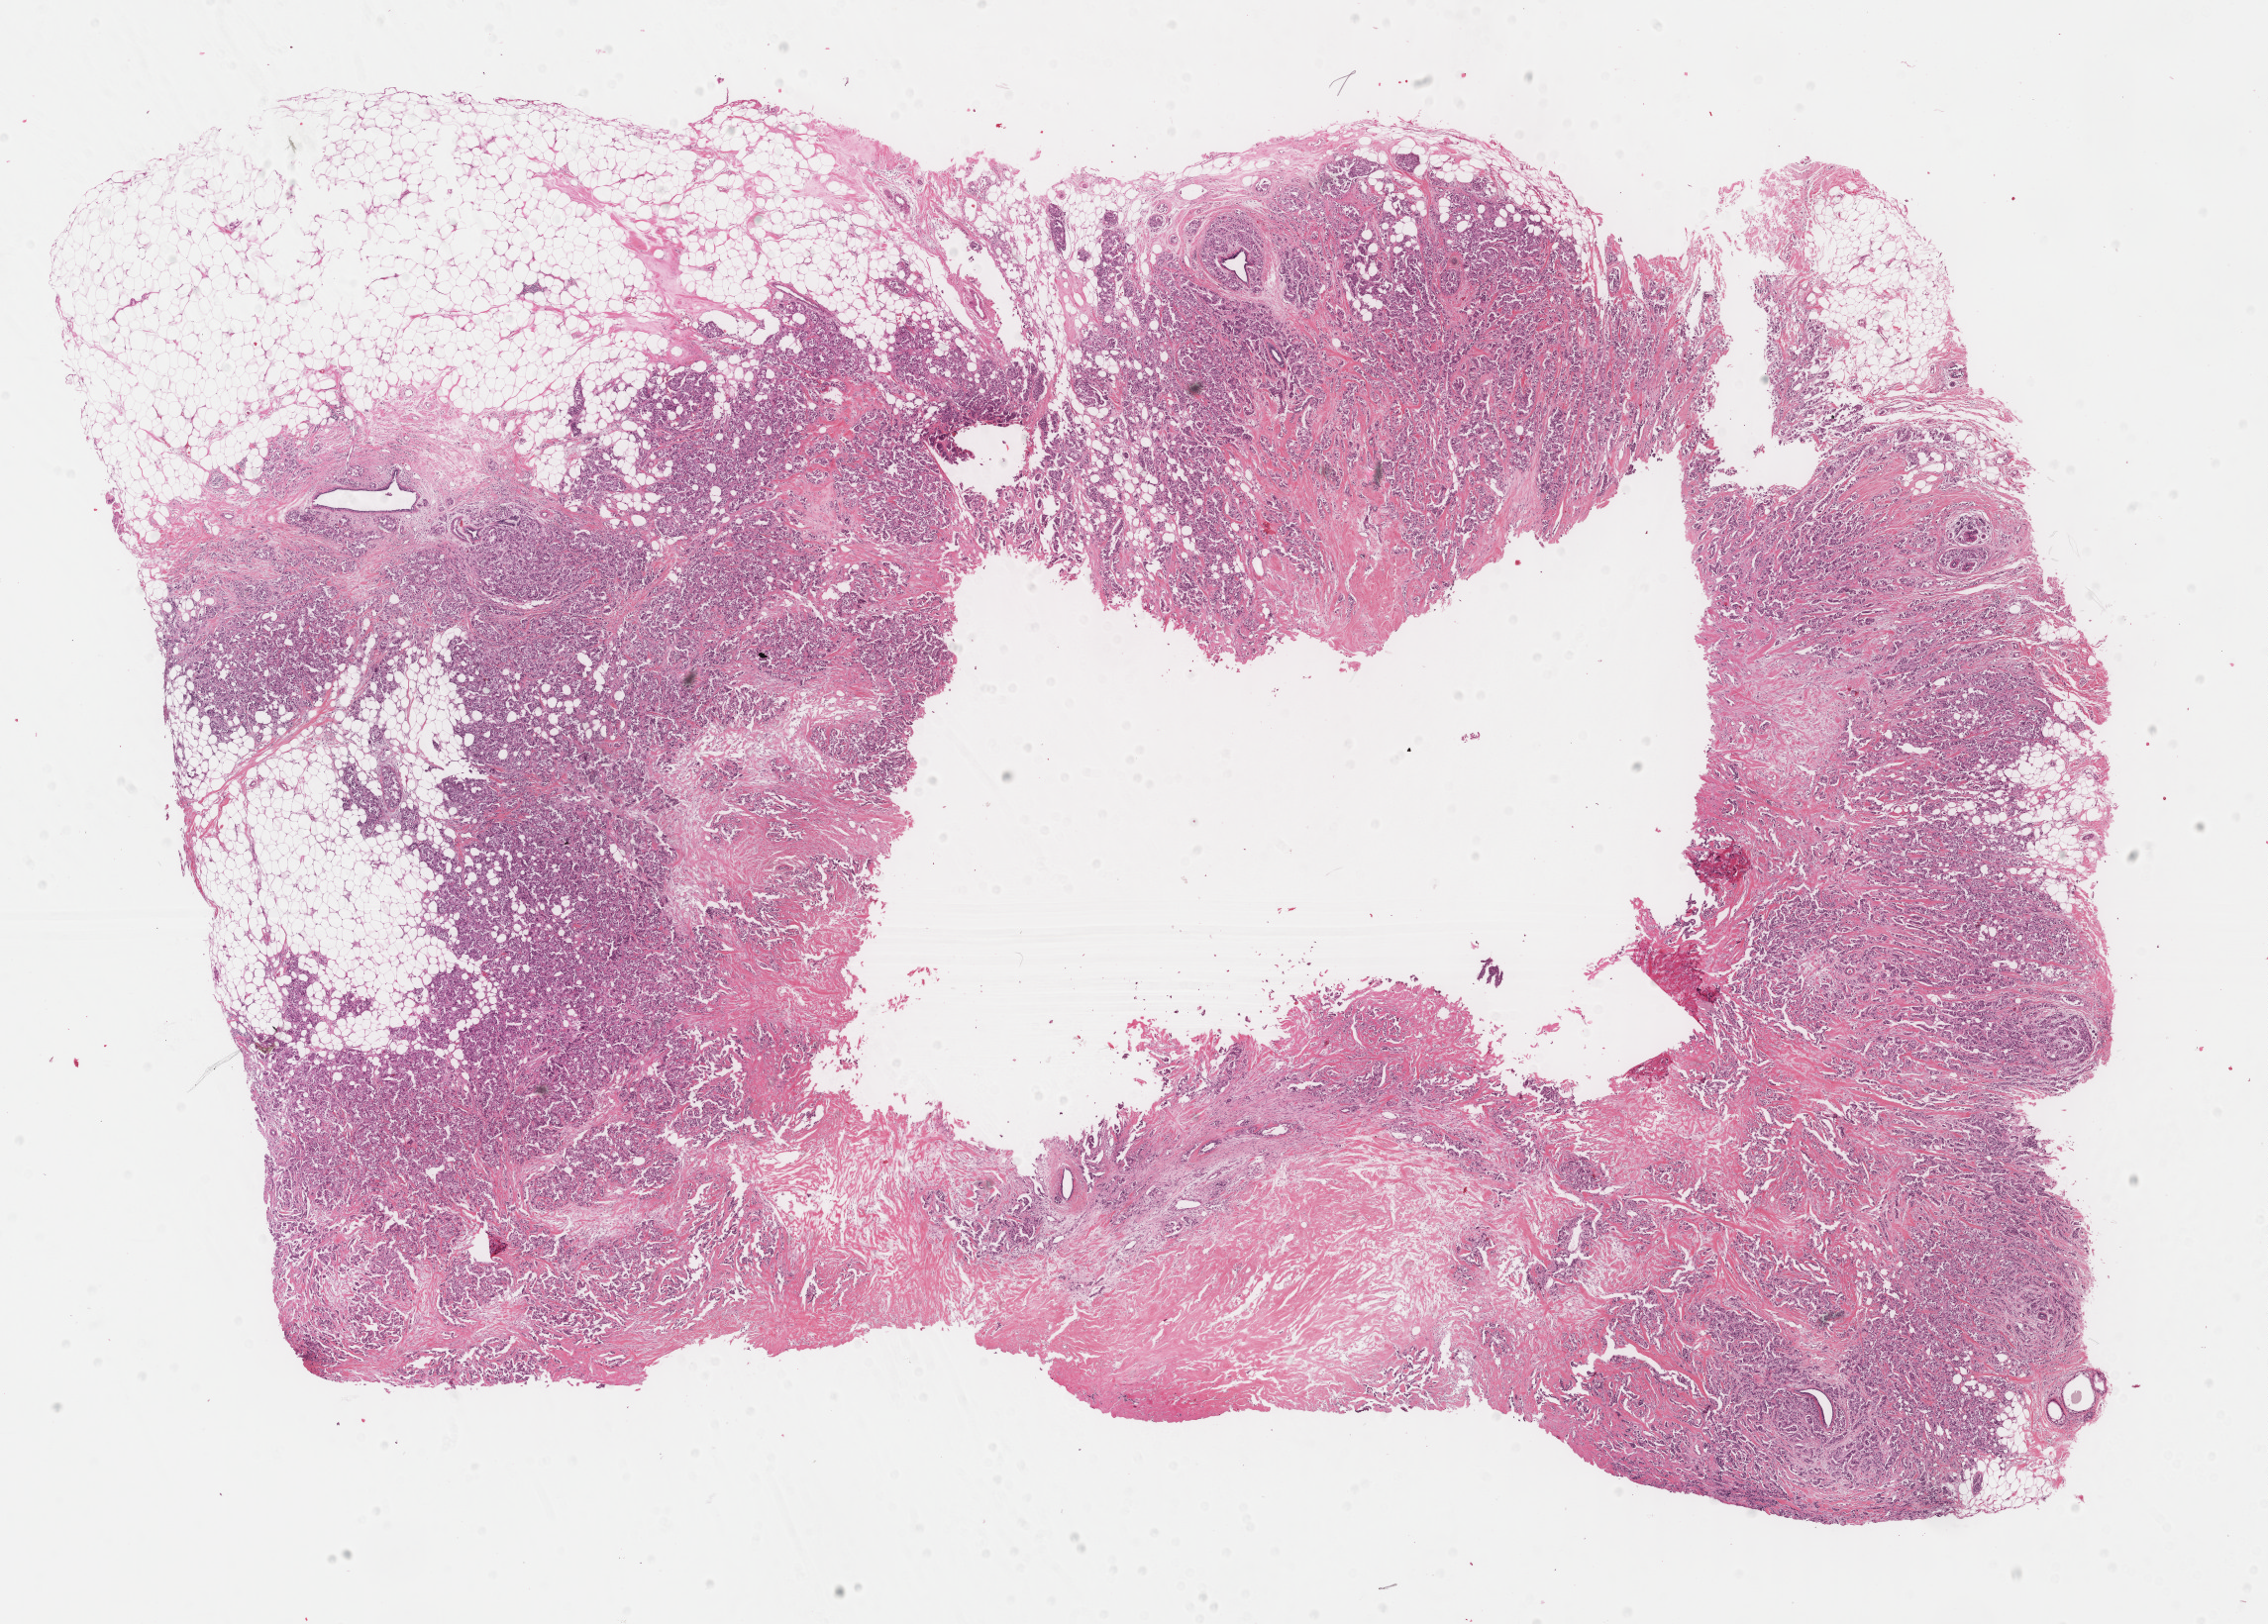
Whole-slide histology image, Hematoxylin and eosin (H&E) stained, low-resolution overview of the scanned area, about 18.2 x 13.0 mm (from a 40x scan). Formalin-fixed paraffin-embedded (FFPE) diagnostic section. Breast, primary tumour sample. Female, age 58 years at initial diagnosis.
Lymph nodes positive (case pathology): 0 of 12 examined. Diagnosis: Infiltrating duct carcinoma, NOS. AJCC pathologic stage: IIA.